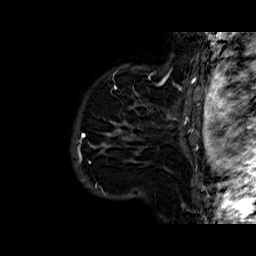
Breast MRI (dynamic contrast-enhanced), one sagittal slice. Position 50 of 60 along the scan axis. Dynamic contrast-enhanced series, time point 2 of 6 at this slice position (early post-contrast). 1.5 T. TE 6.4 ms, TR 32.8 ms. 4 mm slice thickness. 256 × 256 image matrix. Female patient. From the clinical record (not read from this slice): setting: breast cancer imaged before/during neoadjuvant chemotherapy; receptor status: HR-positive, HER2-negative.
Annotated regions visible in this slice (semi-automatic segmentation, software-assisted and operator-edited):
- analysis volume of interest (the breast-tissue region the enhancement analysis was run in; not a lesion): bounding box [x1, y1, x2, y2] px = [86, 77, 163, 164]
- tumour enhancement mask (voxels above the 100 % enhancement threshold inside the analysis volume of interest): [107, 129, 132, 136]